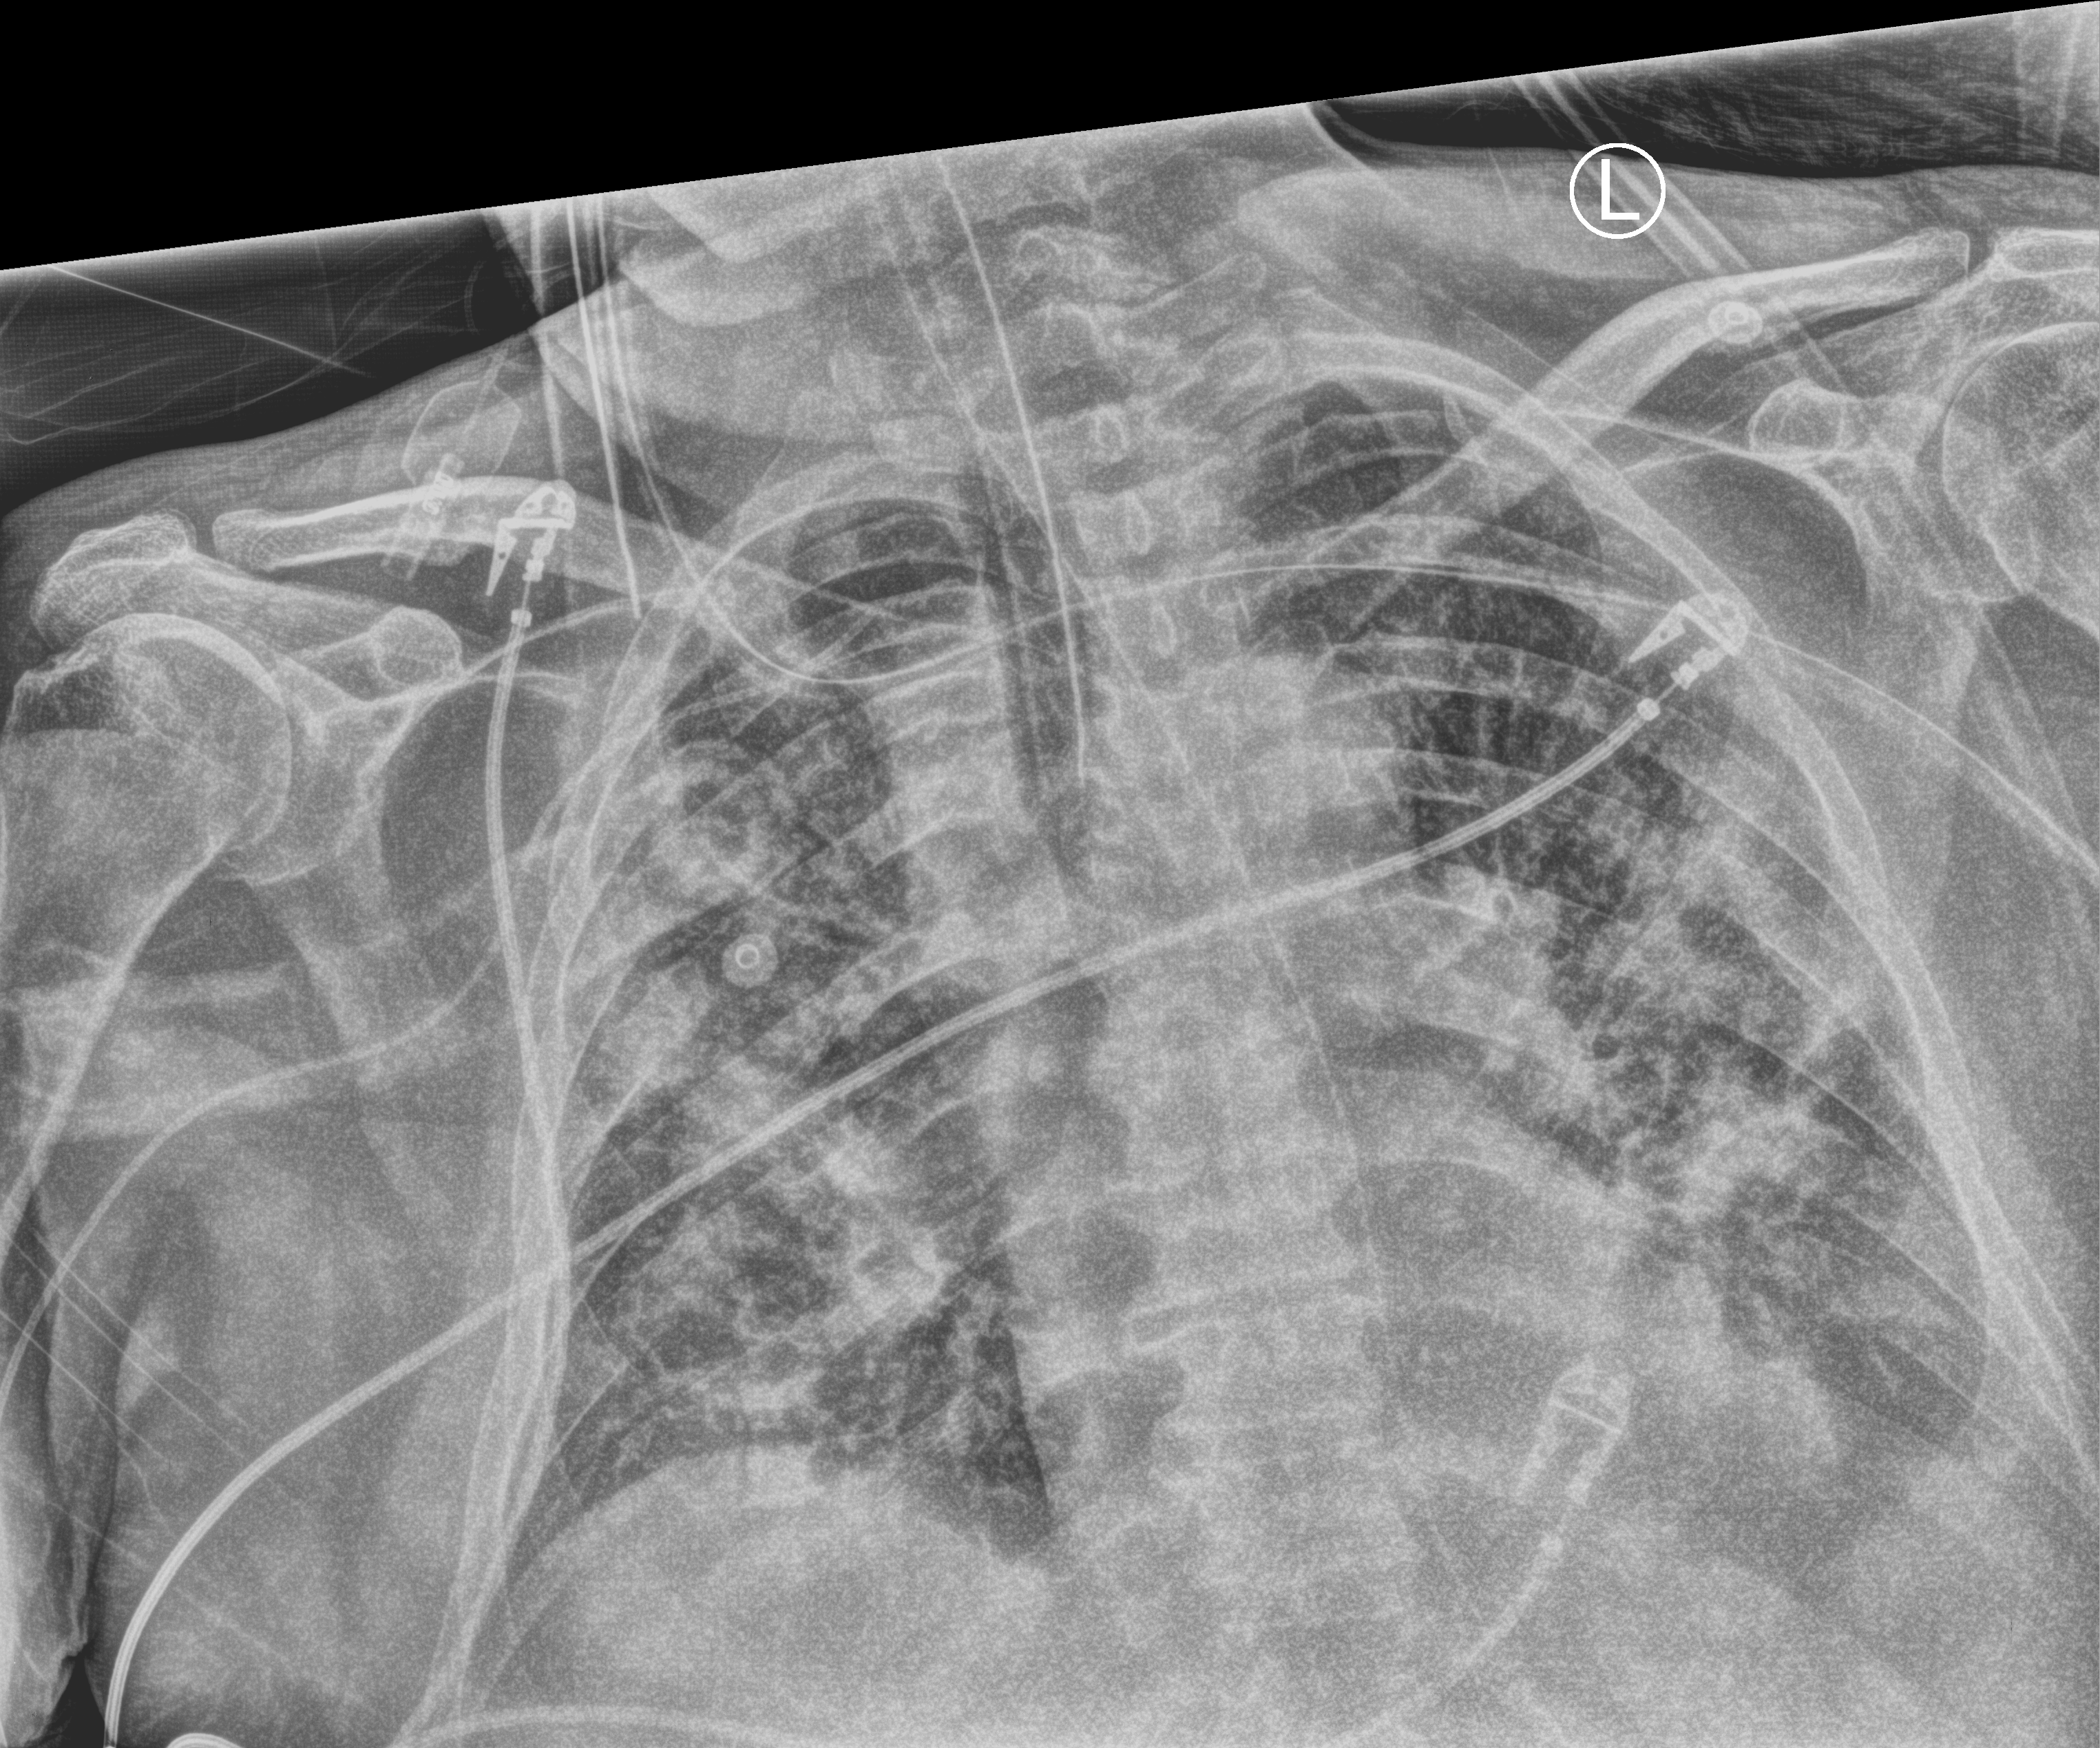
Portable chest radiograph; anteroposterior (AP) projection. Male patient hospitalised with COVID-19, age 60–74 years.
From the hospital-stay record, not from the radiograph (when in the stay this image was taken is not recorded): admitted to intensive care during this hospital stay: yes.